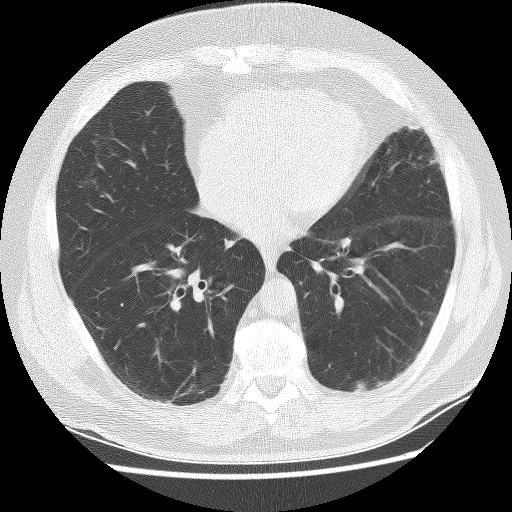
Axial slice from a low-dose chest CT screening exam, first (baseline) screen, lung window (W 1500 / L -600 HU), 2.5 mm slice thickness, 512 × 512 image matrix, field of view 340 × 340 mm. Male participant, aged 65 years at enrolment. Former smoker at enrolment.
Expert-annotated lung lesion, bounding box <351,370,391,405> (left, top, right, bottom; pixels). Screening reader's record for this exam: no non-calcified nodule ≥4 mm recorded. Official screen result: negative screen, minor abnormalities not suspicious for lung cancer. Later outcome: lung cancer diagnosed 523 days after this screen — squamous cell carcinoma, NOS, left lower lobe, moderately differentiated (G2), stage IA (AJCC 6th edition), 20 mm at pathology.